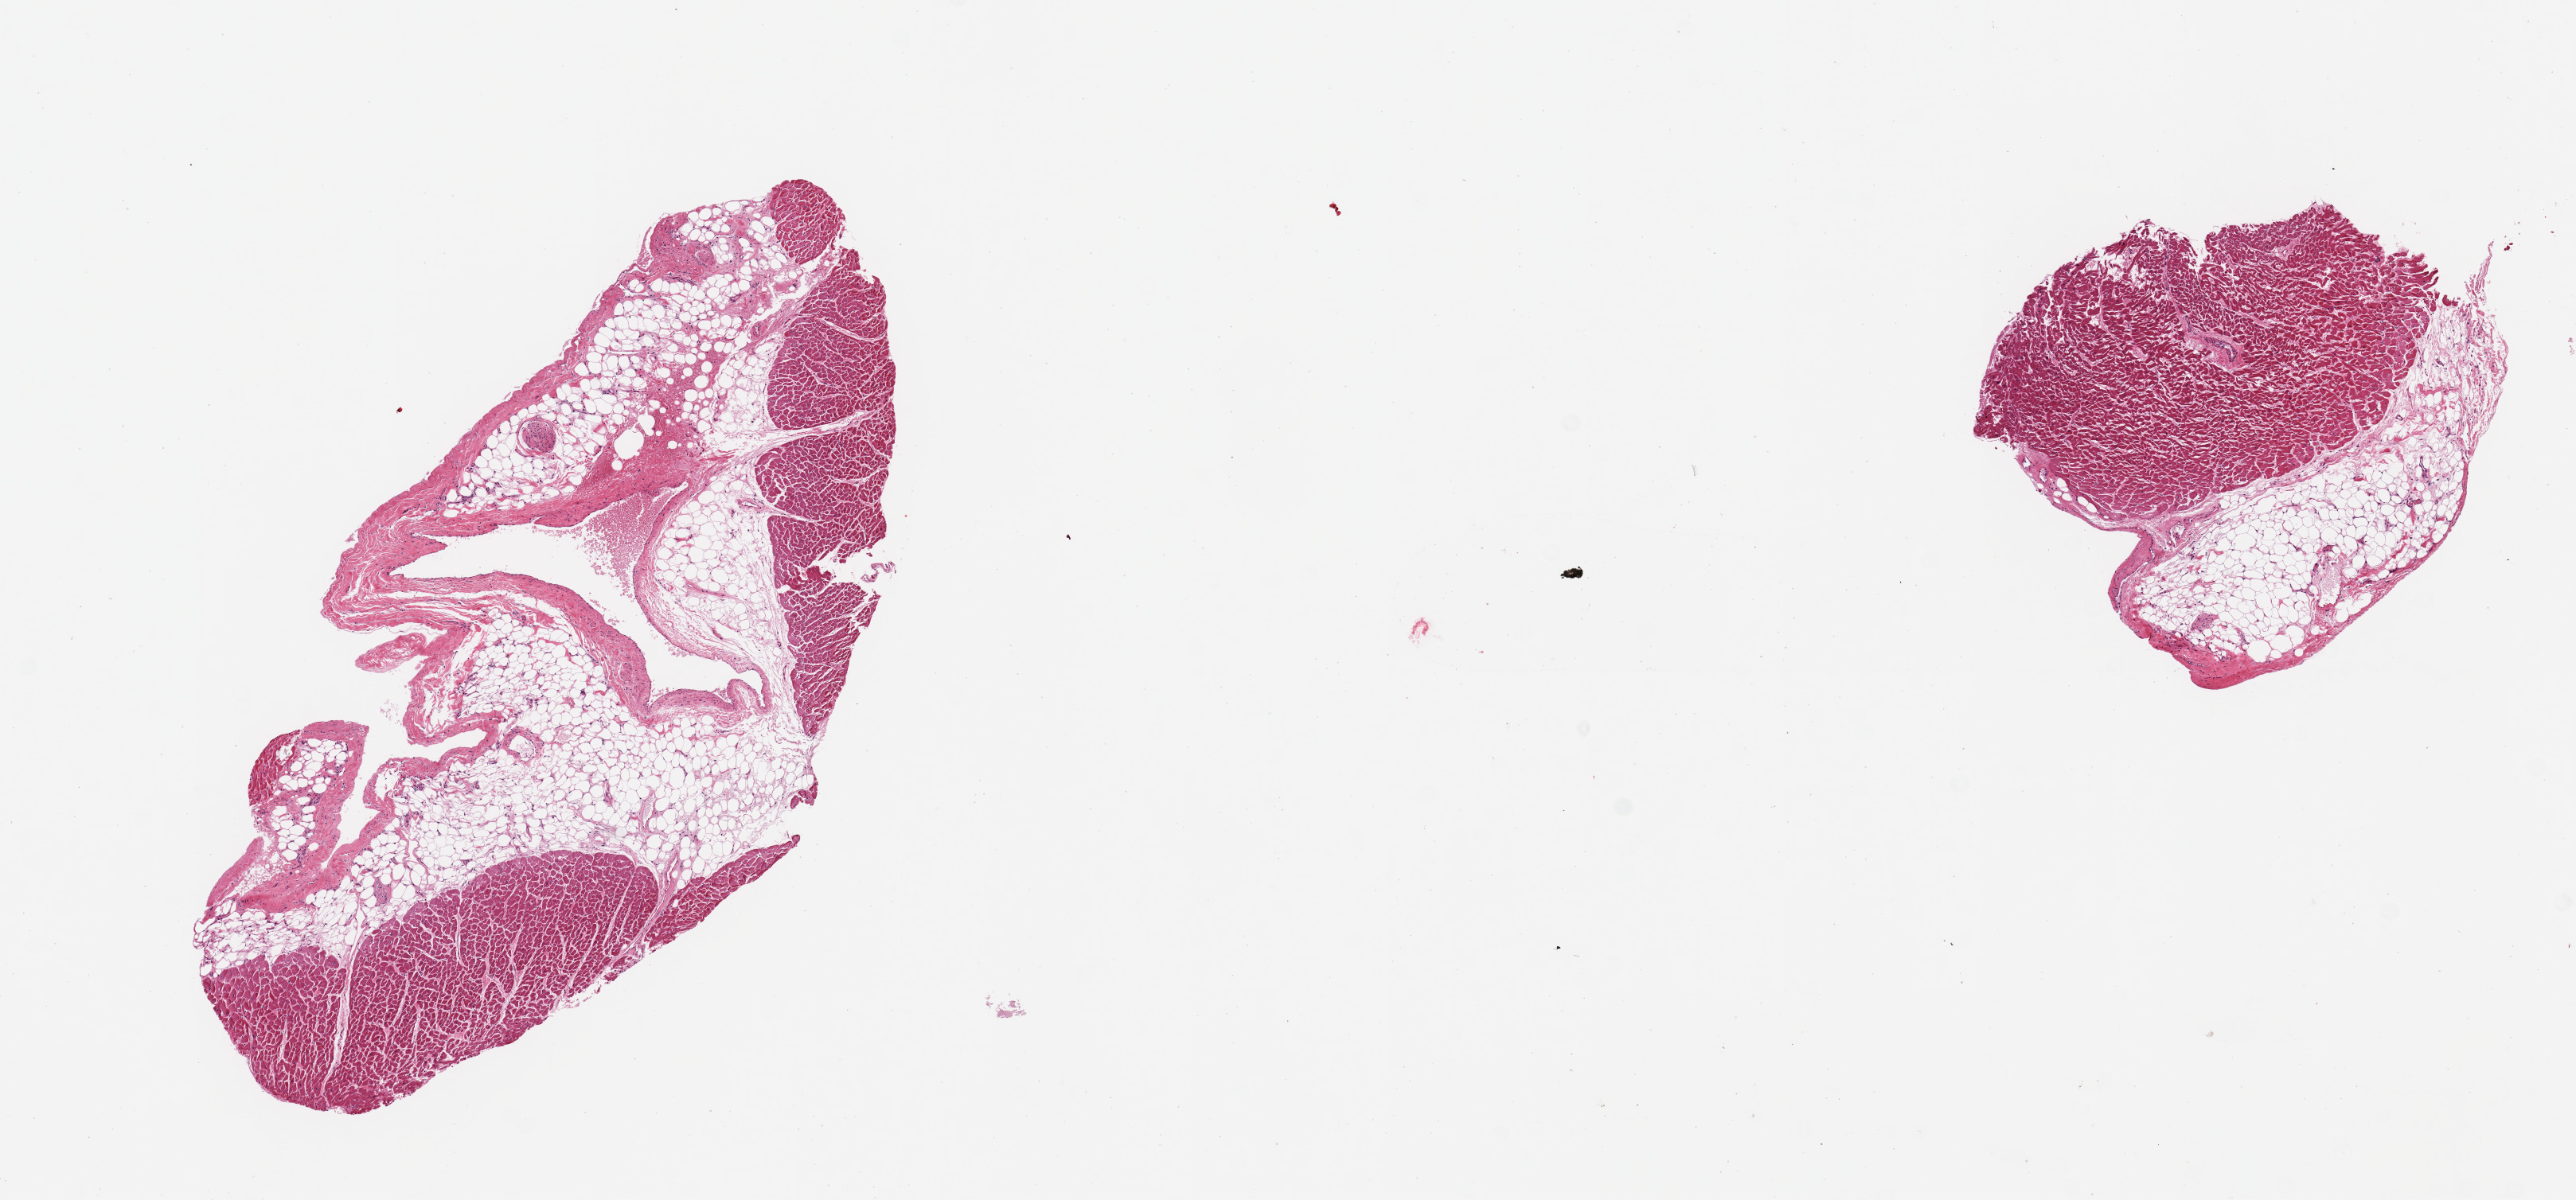
Whole-slide image, hematoxylin and eosin (H&E) stain, brightfield — a low-resolution overview of the entire scanned area, about 12.8 x 6.0 mm; PAXgene-fixed, paraffin-embedded tissue; section of coronary artery (target tissue); tissue donor sample. Donor: male.
• reviewer comment on this tissue sample: 2 pieces; vein, myocardium, and fat